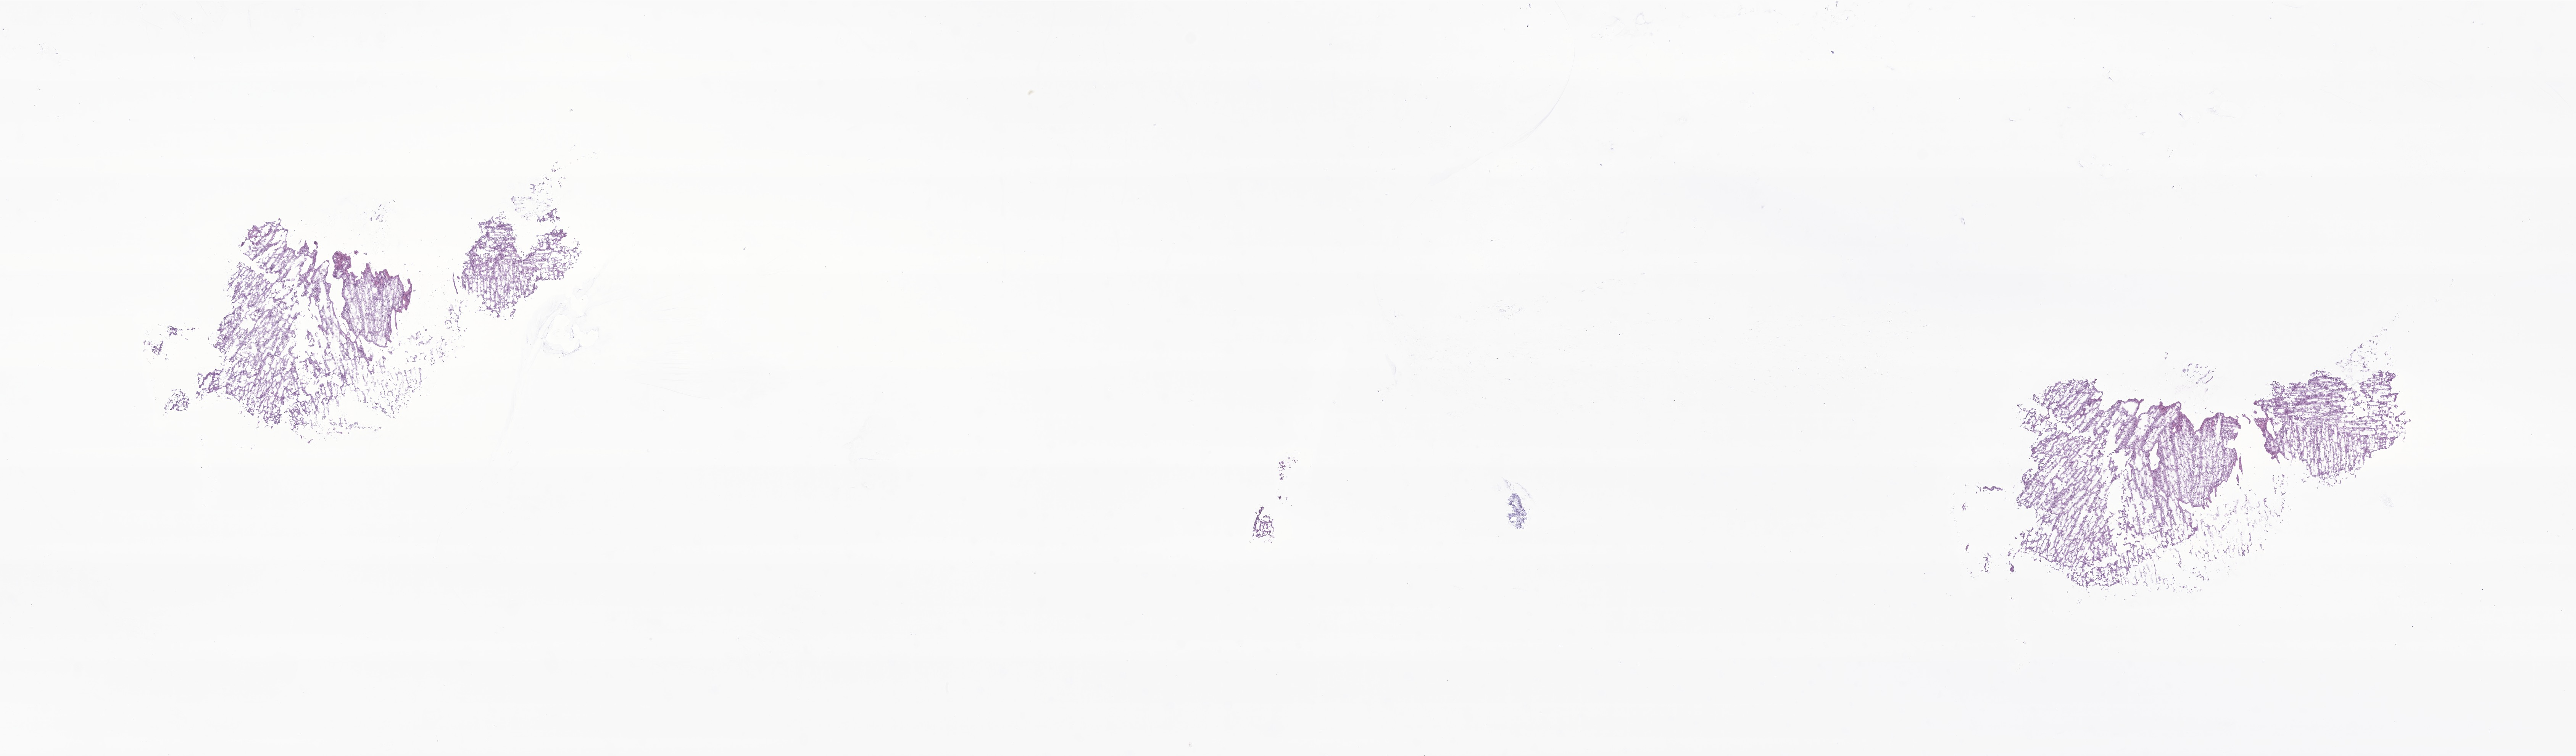
Hematoxylin and eosin (H&E) whole-slide image of tumor tissue from the brain — a low-resolution overview of the entire scanned area, about 28.5 x 8.4 mm. Frozen section (OCT-embedded). Male patient, age 96 days.
Diagnosis (ICD-O-3 morphology term): Glioma, malignant.